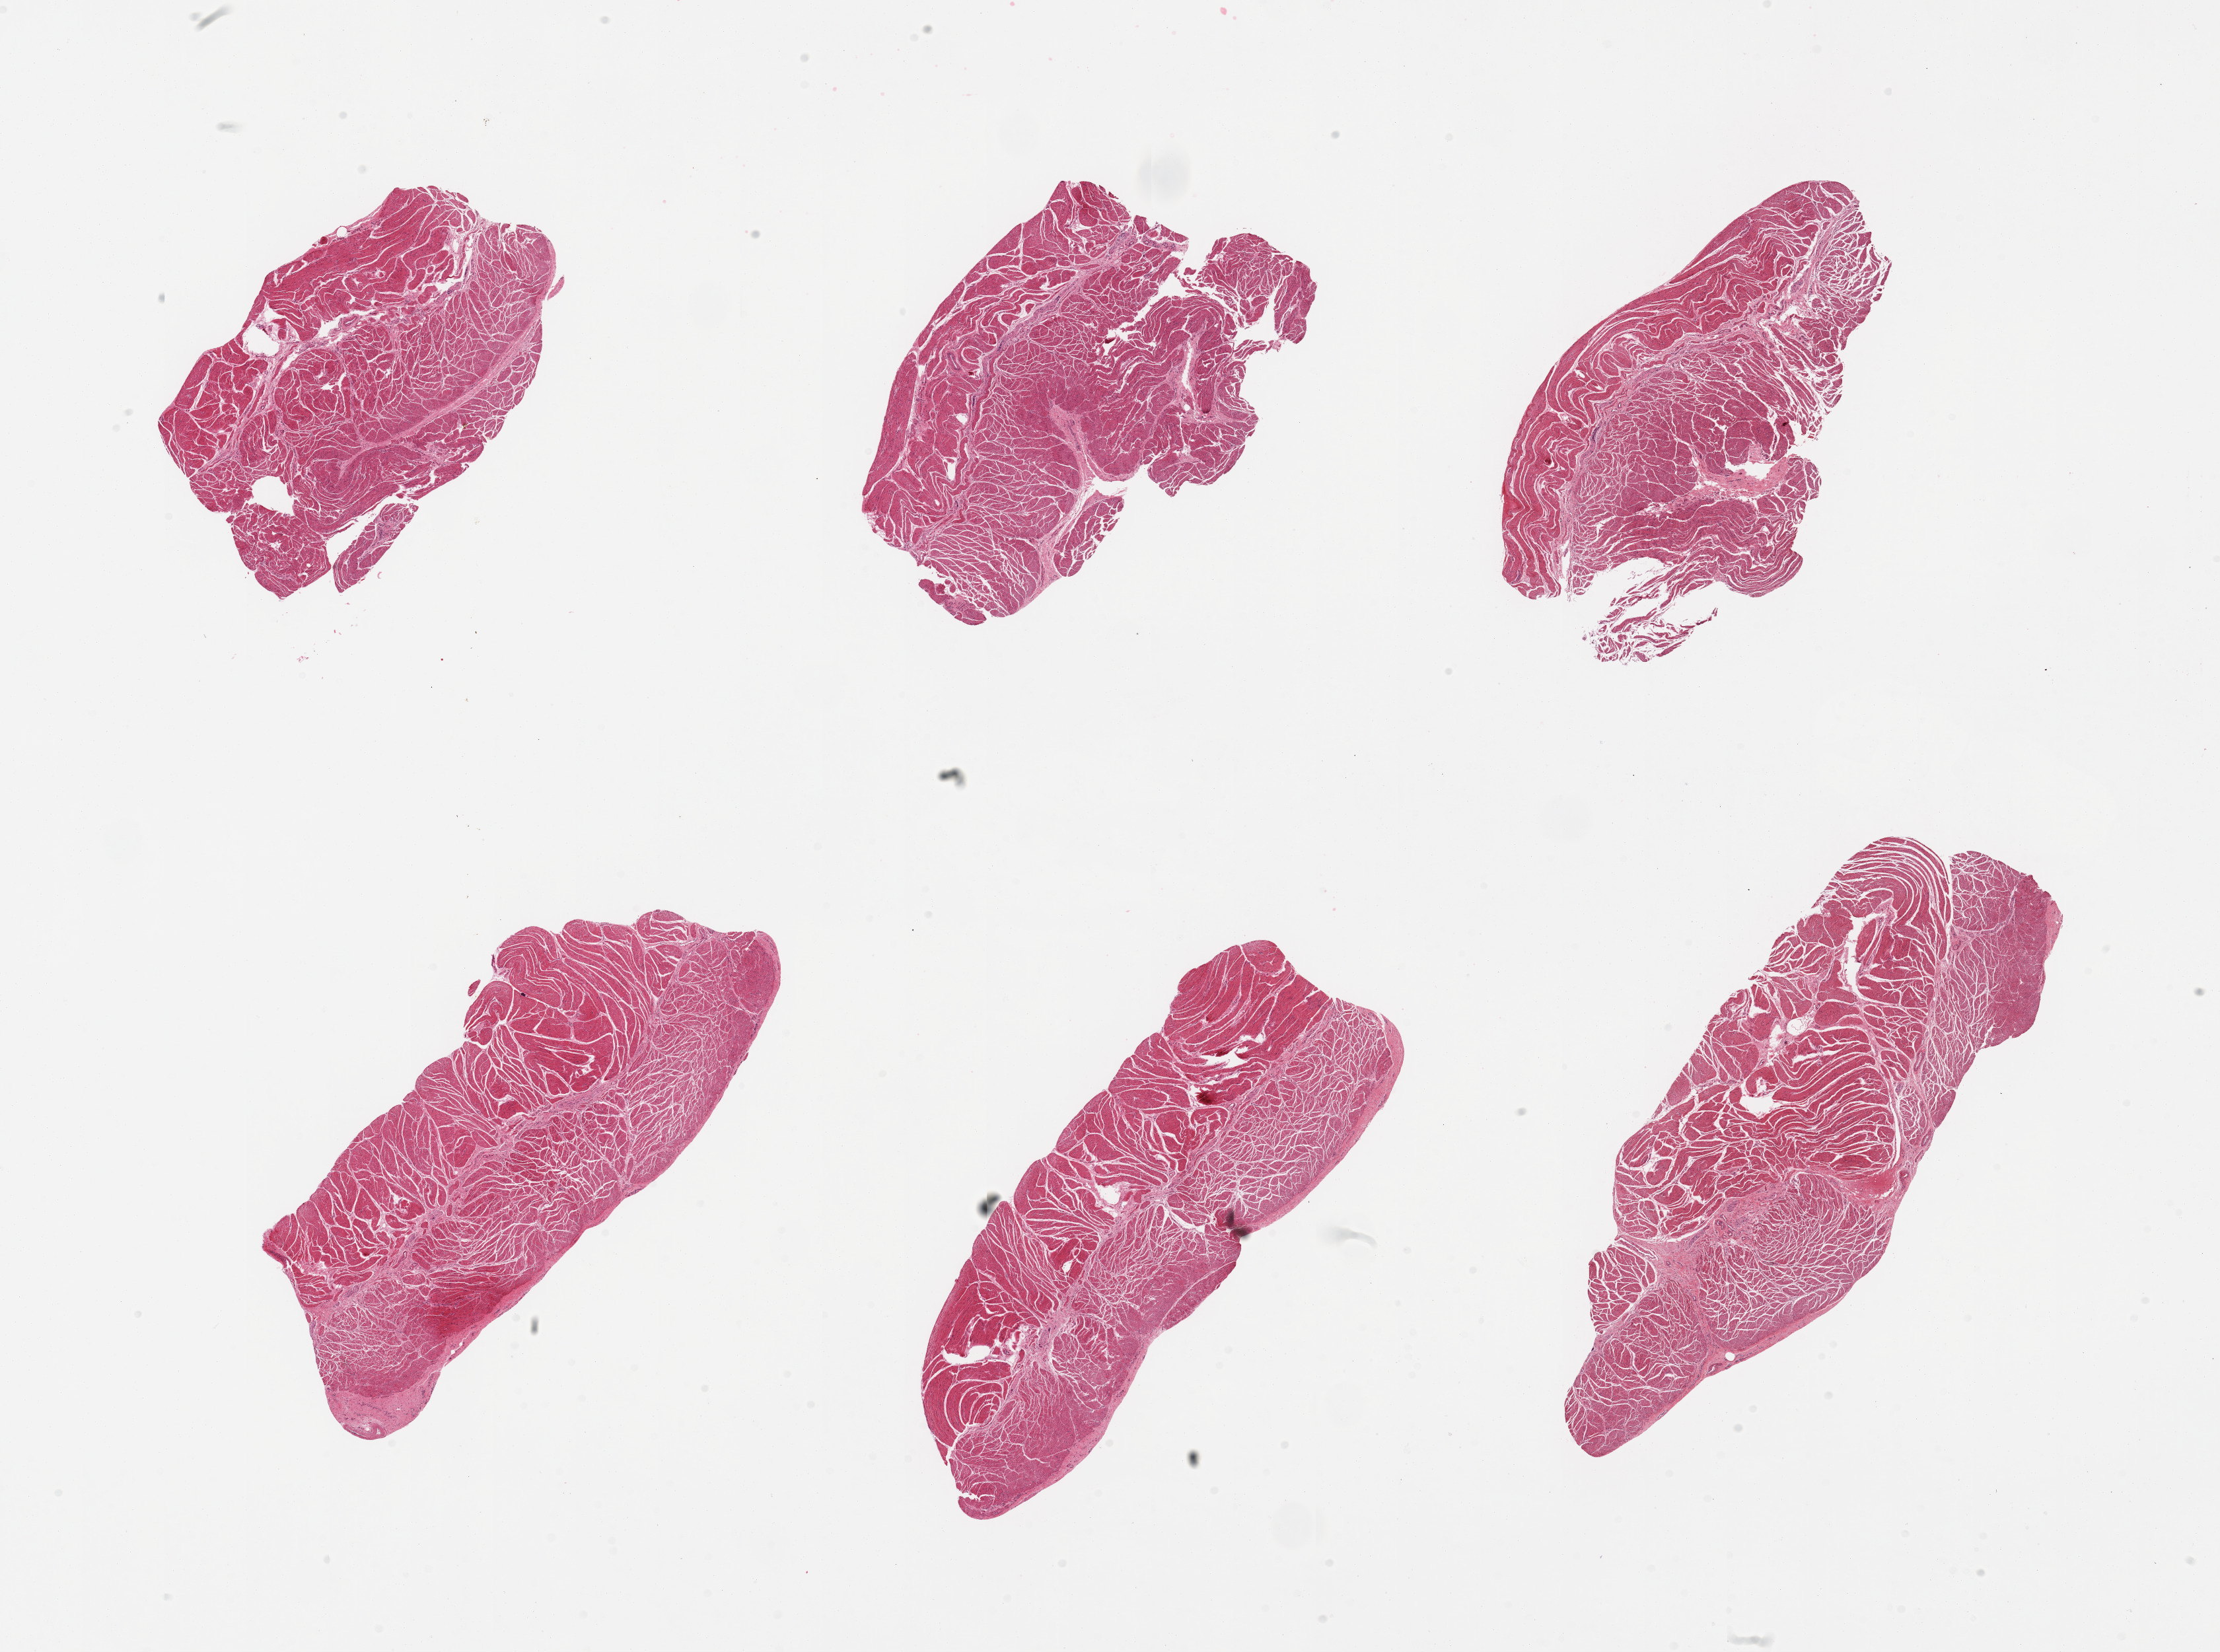
H&E whole-slide image — shown as a low-resolution overview of the whole scanned area (about 26.6 x 19.8 mm, slide scanned at 20x); PAXgene-fixed paraffin-embedded (PFPE) section; sampled site (target tissue): esophageal muscle; tissue donor sample. Donor: female.
- review note (as recorded): 6 pieces; well trimmed